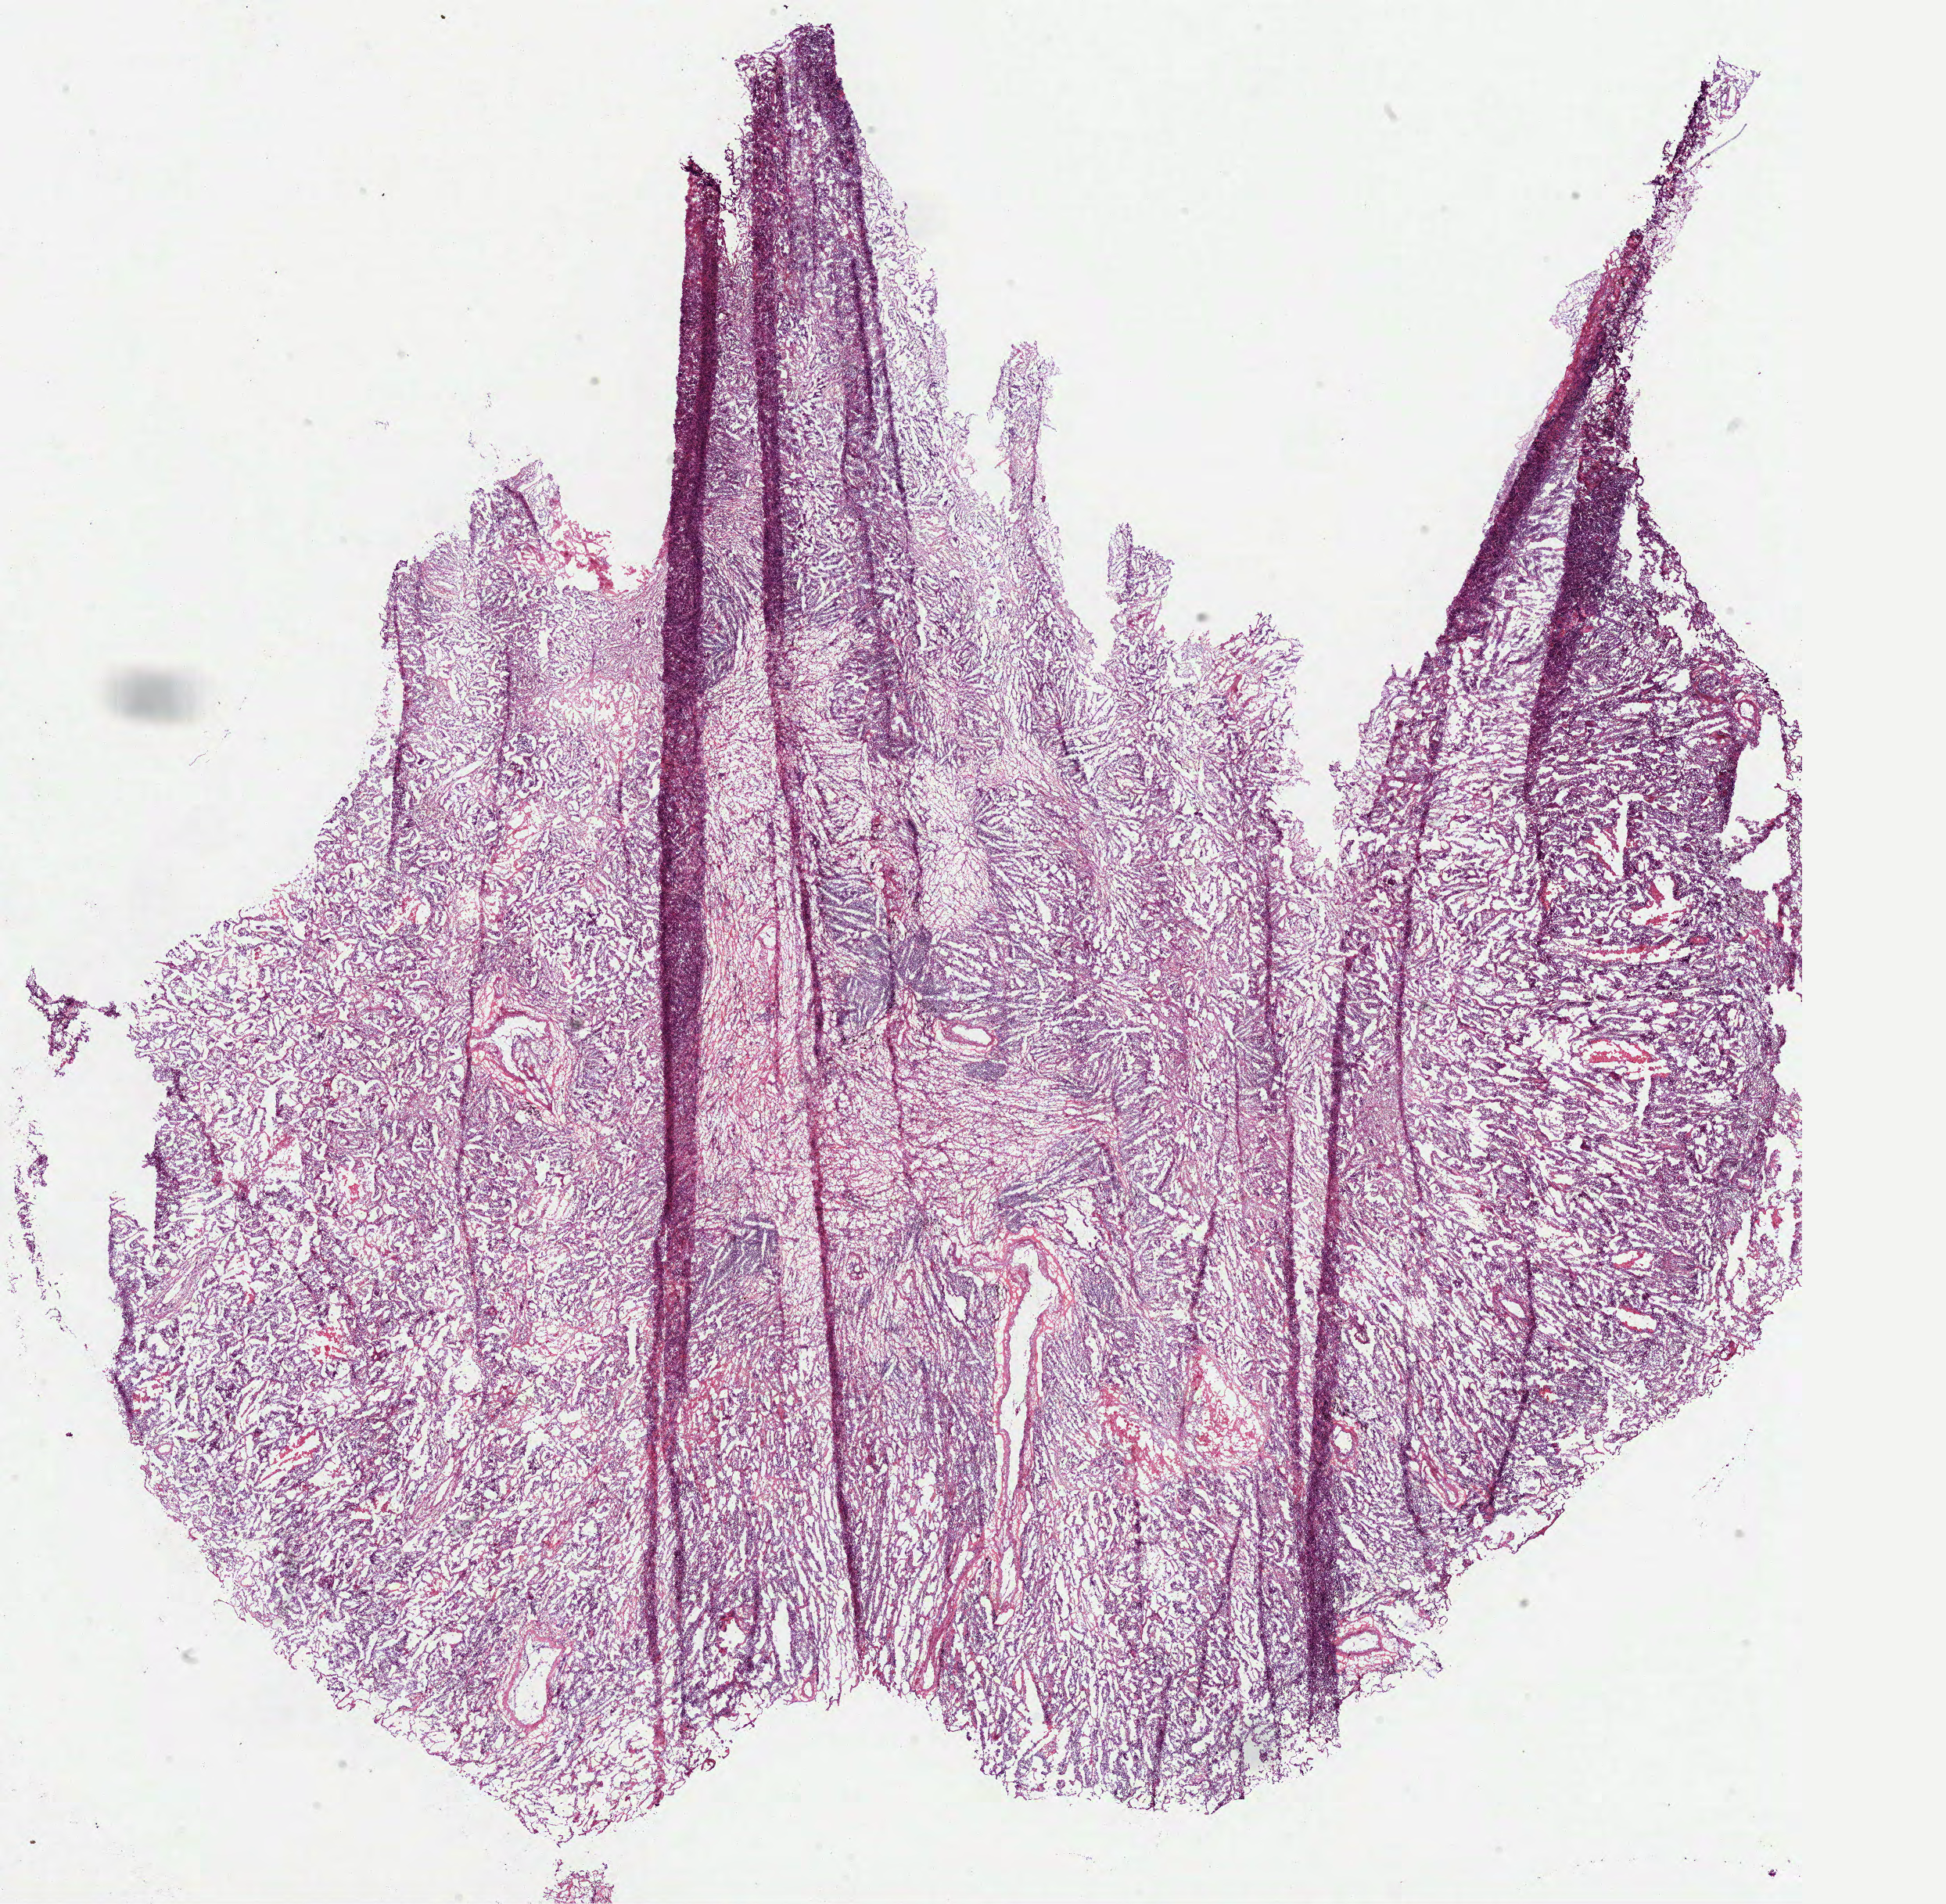
Digitized Hematoxylin and eosin (H&E) stained tissue section (whole slide) — whole scanned area (about 20.1 x 19.6 mm) shown as a low-resolution overview; frozen section from the bottom of the tissue portion; sample: primary tumour, lung. Male patient; age at initial diagnosis 57 years. Slide review estimates, as recorded: tumour cells 80%, tumour nuclei 75%, normal cells 0%, stromal cells 15%, necrosis 5%.
Pathologic diagnosis: Solid carcinoma, NOS. Laterality: left. AJCC pathologic stage: IB (7th edition).